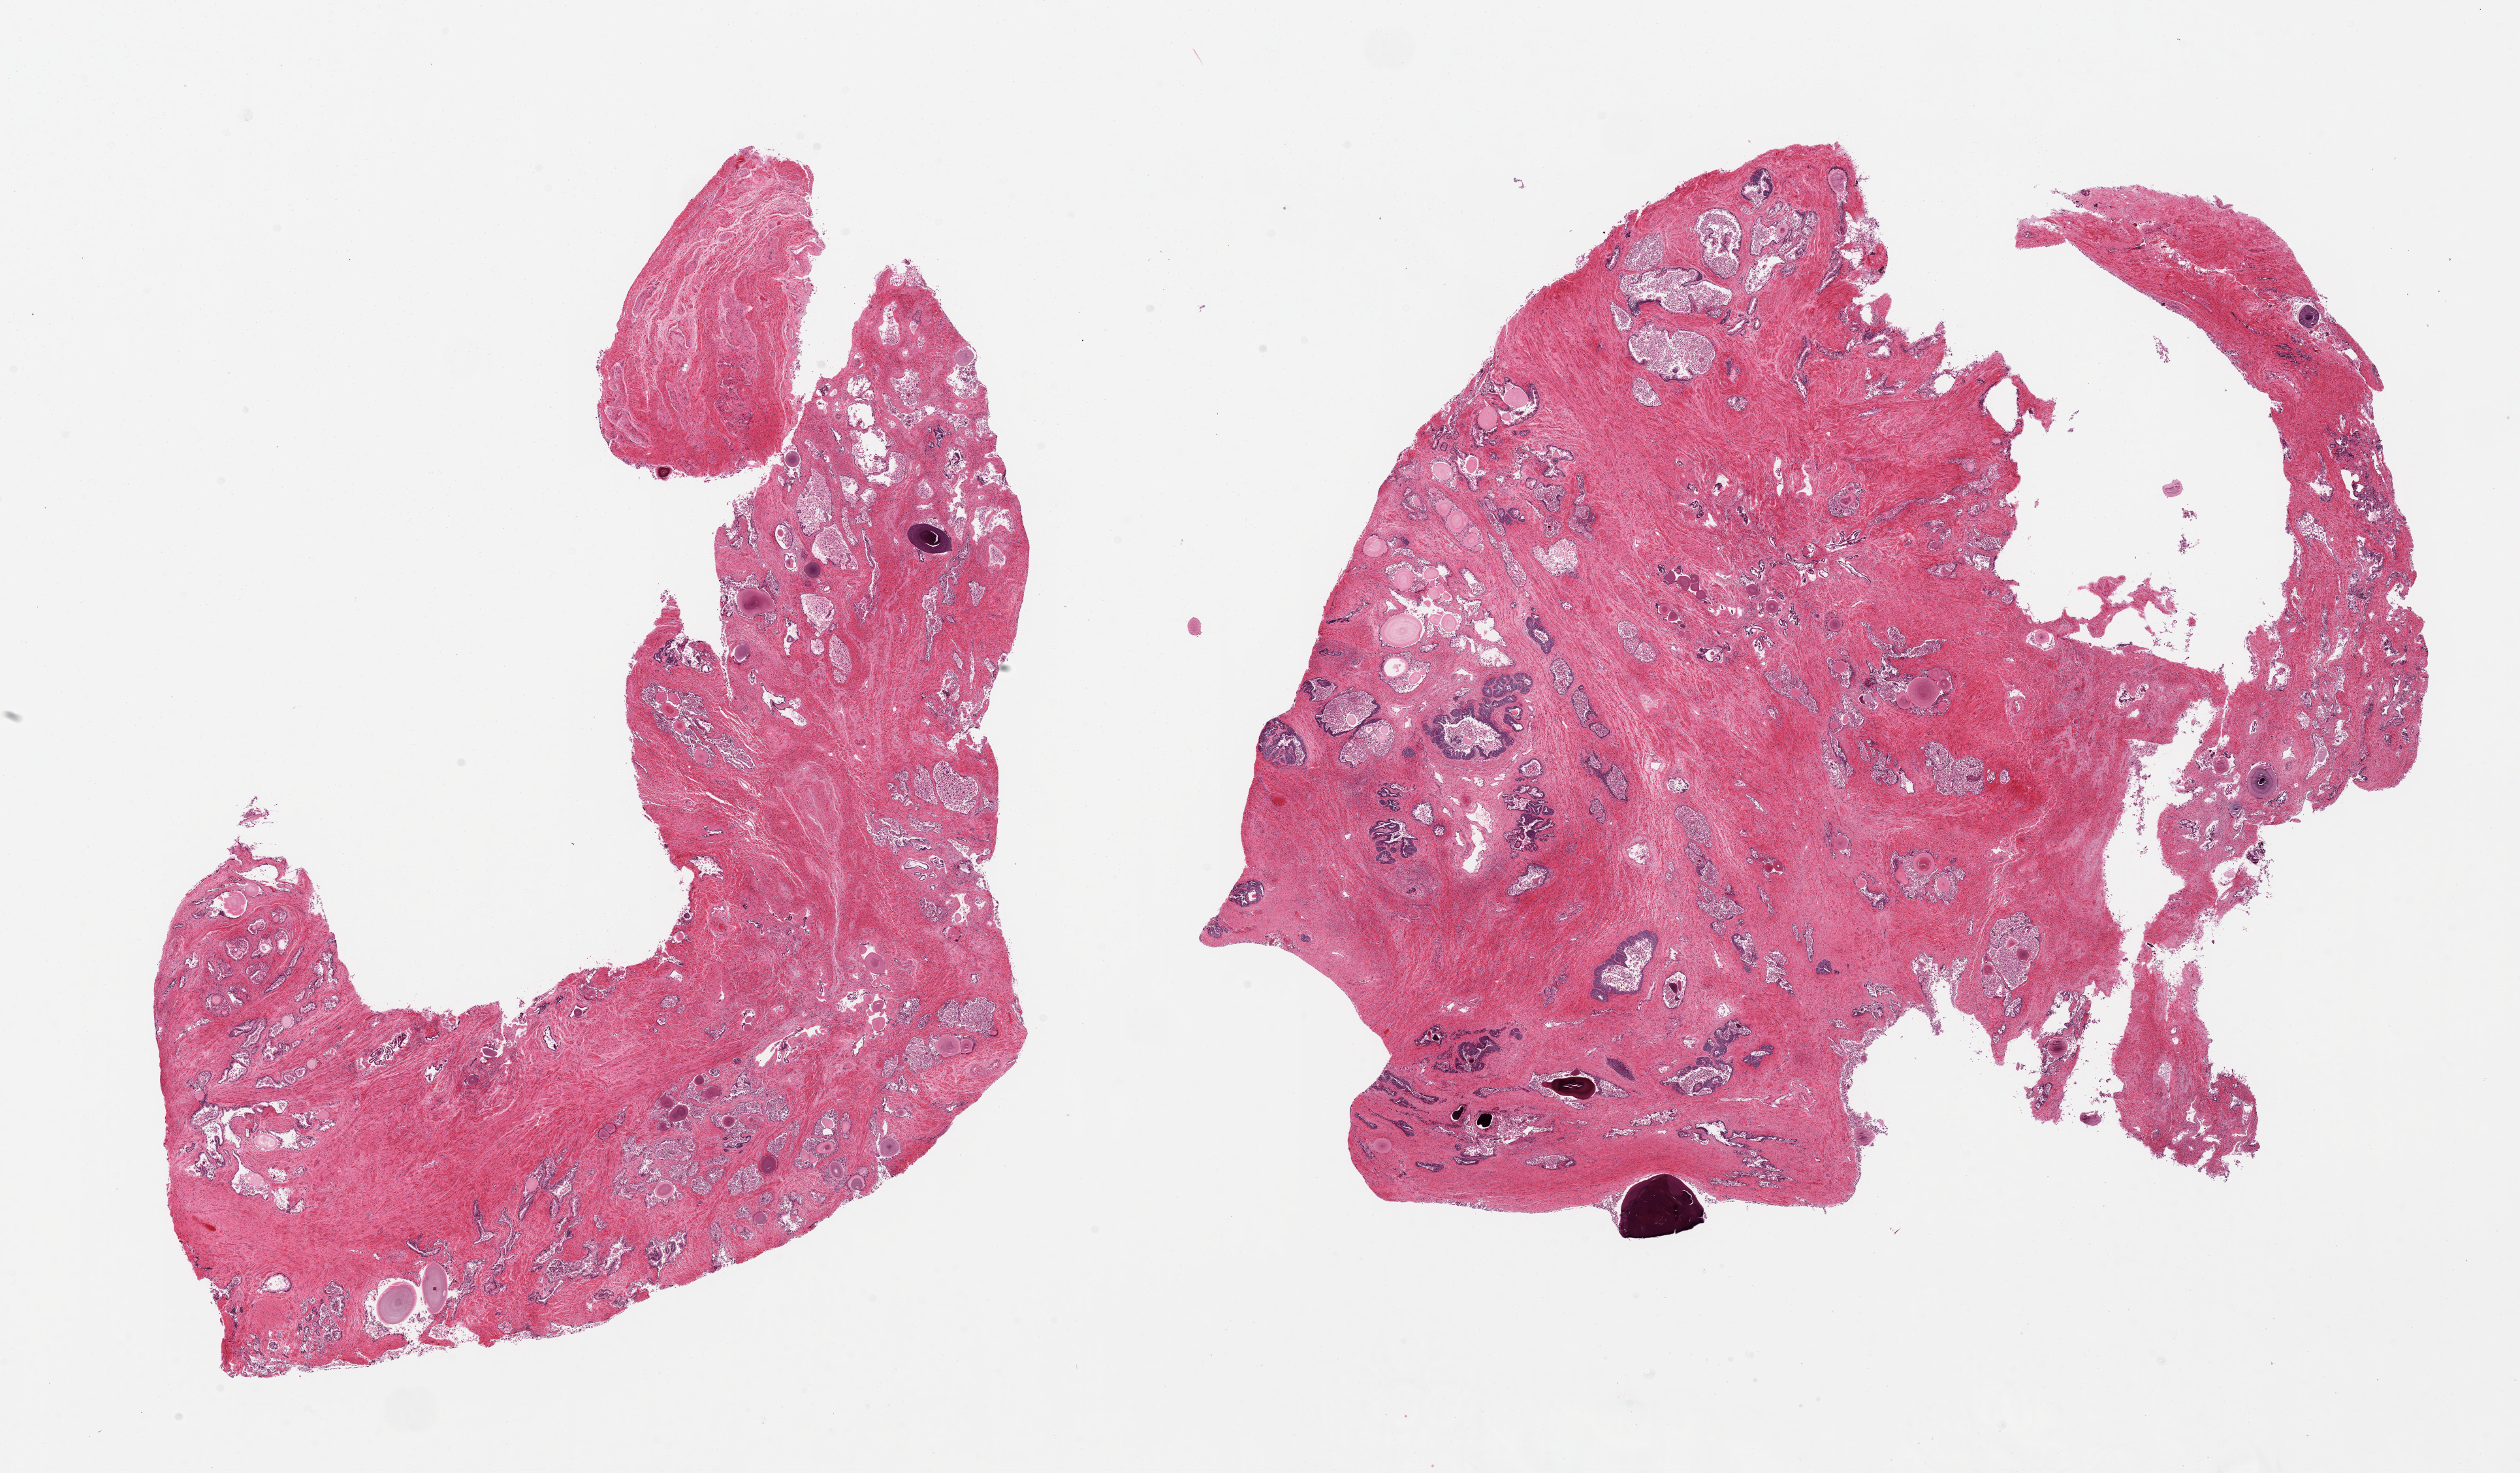
Digitized H&E-stained section — shown as a low-resolution overview of the whole scanned area (about 30.5 x 17.8 mm, from a 20x scan); PAXgene-fixed, paraffin-embedded tissue; sampled site (target tissue): prostate; donor tissue sample. Male donor.
Pathologist's review note for this sample: 2 irregular pieces, numerous corpora amylacea/prostatic concretions, epithelium sloughing, basal cell hyperplasia.